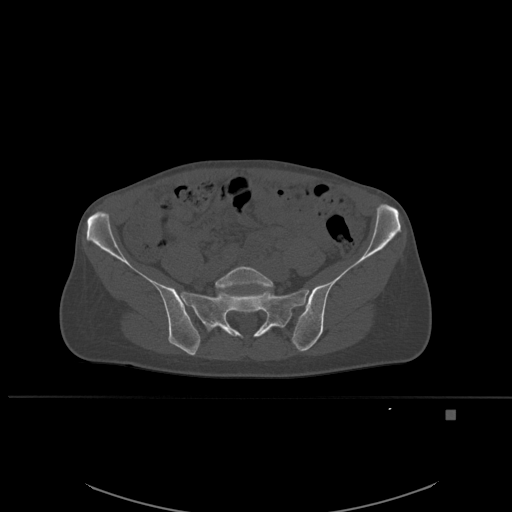
CT including the spine, one axial slice; position 160 of 537 along the scan axis; bone window (W 1800 / L 400 HU); 1.5 mm slice thickness; 512 × 512 image matrix, field of view 440 × 440 mm. Female patient, age 45 years. From the clinical record (not read from this slice): primary cancer: lung.
Annotated regions visible in this slice (semi-automatic segmentation, software-assisted and operator-edited):
- L5 vertebra: bounding box <215,266,273,290> (left, top, right, bottom; pixels)